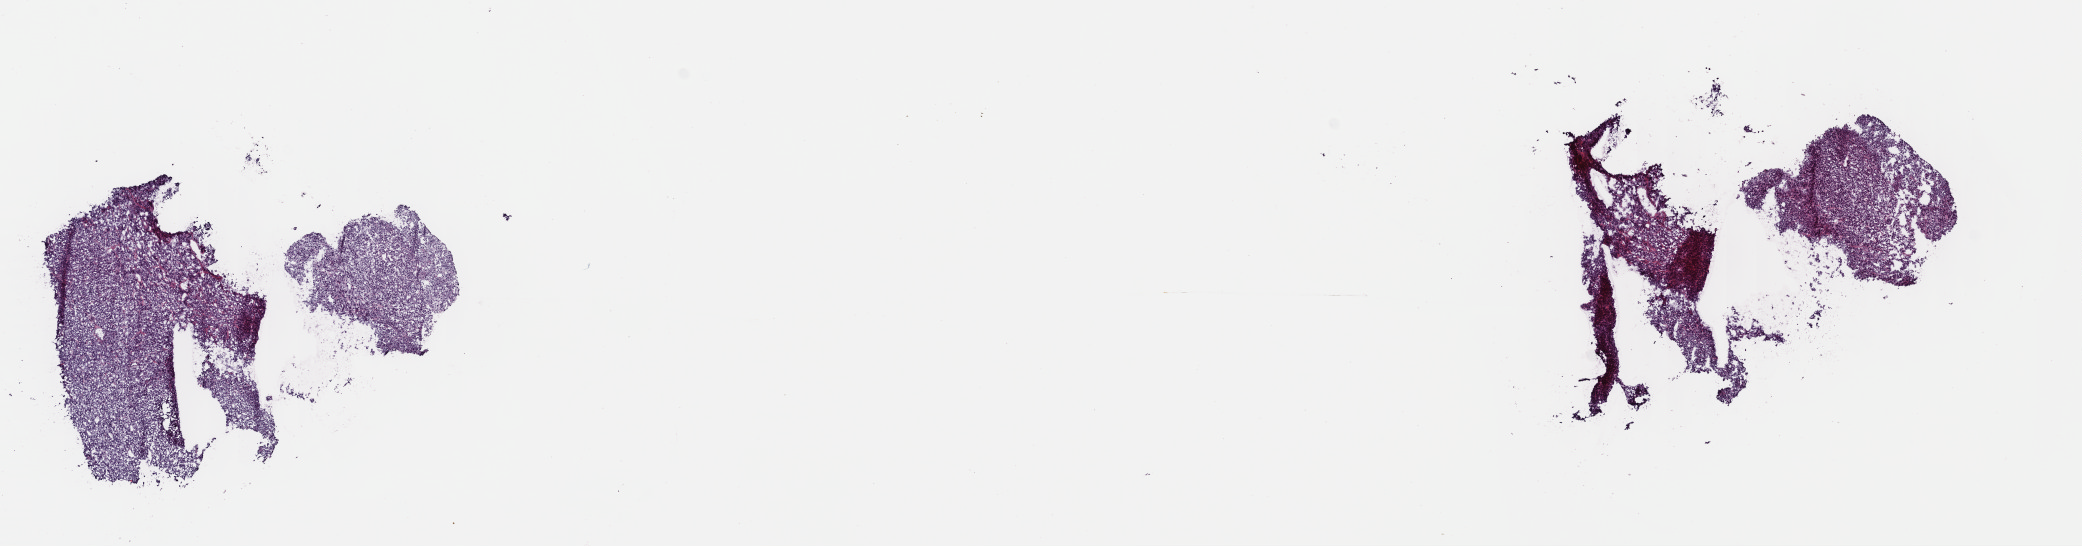
Whole-slide histology image, H&E, shown as a low-resolution overview of the whole scanned area (about 16.4 x 4.3 mm, from a 40x scan), frozen section from the top of the tissue portion, adrenal cortex, primary tumour sample. Patient: female, age at initial diagnosis 30 years. Composition of this section per pathologist review: tumour cells 100%, tumour nuclei 95%, normal cells 0%, stromal cells 0%, necrosis 0%. Infiltration values recorded for this section: lymphocyte infiltration 0%, monocyte infiltration 0%, neutrophil infiltration 0%.
Diagnosis: Adrenal cortical carcinoma (cortex of adrenal gland). Laterality: left.